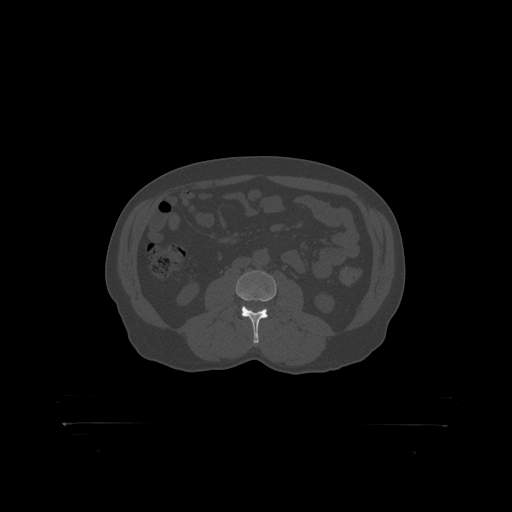
CT including the spine, one axial slice; position 262 of 399 along the scan axis; bone window (W 1800 / L 400 HU); 1.25 mm slice thickness; 512 × 512 image matrix, field of view 650 × 650 mm. Patient: male, 46 years. Case-level facts recorded for this patient, not image findings: primary cancer: skin.
Outlined on this slice (semi-automatic segmentation, software-assisted and operator-edited):
- L3 vertebra: bounding box [x1, y1, x2, y2] px = [236, 271, 277, 319]